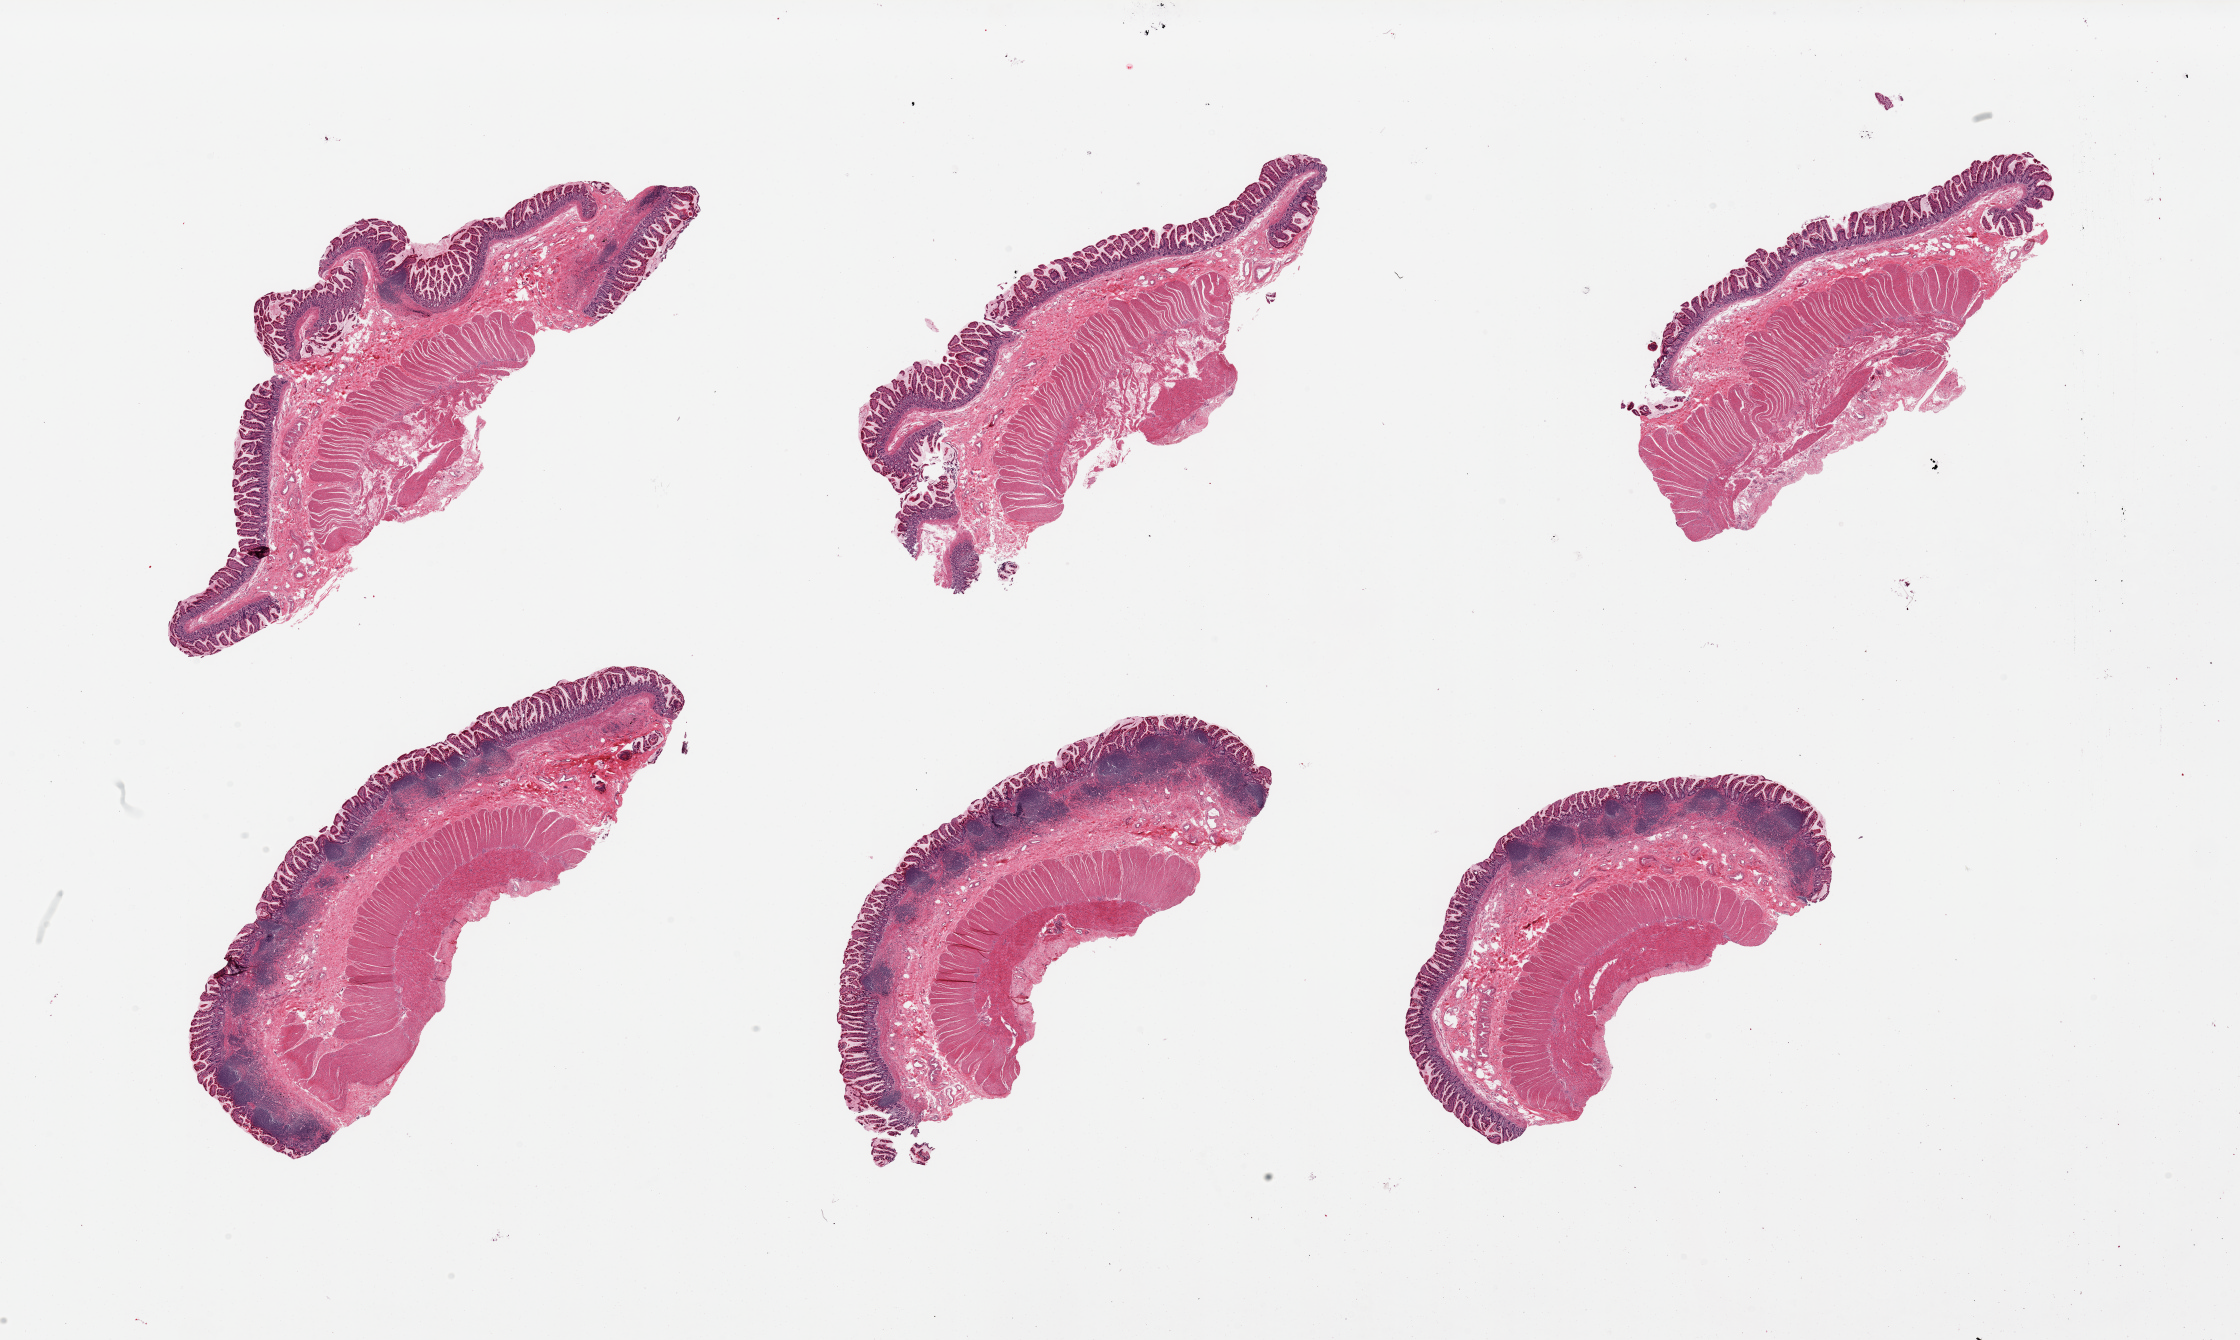
H&E whole-slide image — whole scanned area (about 35.4 x 21.2 mm, from a 20x scan) shown as a low-resolution overview; PAXgene-fixed paraffin-embedded (PFPE) section; target tissue: ileum; donor tissue sample. Donor sex: female.
• pathologist's review note for this sample: 6 pieces; 3 have good lymphoid tissue, BUT all have full thickness muscle as well rather than mucosa only; The muscle makes up over 50% of the pieces; Will be difficult to get lymphoid data